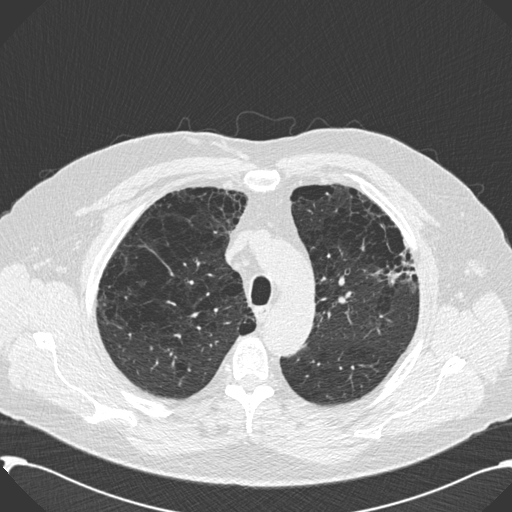
Axial slice from a low-dose chest CT screening exam. Second annual screen. Lung window (W 1500 / L -600 HU). Standard (soft-tissue) reconstruction kernel (B30f). 120 kVp. Male participant, aged 59 years at enrolment.
Expert reader's lesion annotation, bounding box [x1, y1, x2, y2] px = [364, 218, 419, 299]. No non-calcified nodule or mass ≥4 mm was recorded by the screening reader at this exam. Later outcome: lung cancer diagnosed 518 days after this screen — bronchiolo-alveolar carcinoma, mixed mucinous and non-mucinous, left upper lobe, stage IA (AJCC 6th edition), 20 mm at pathology.